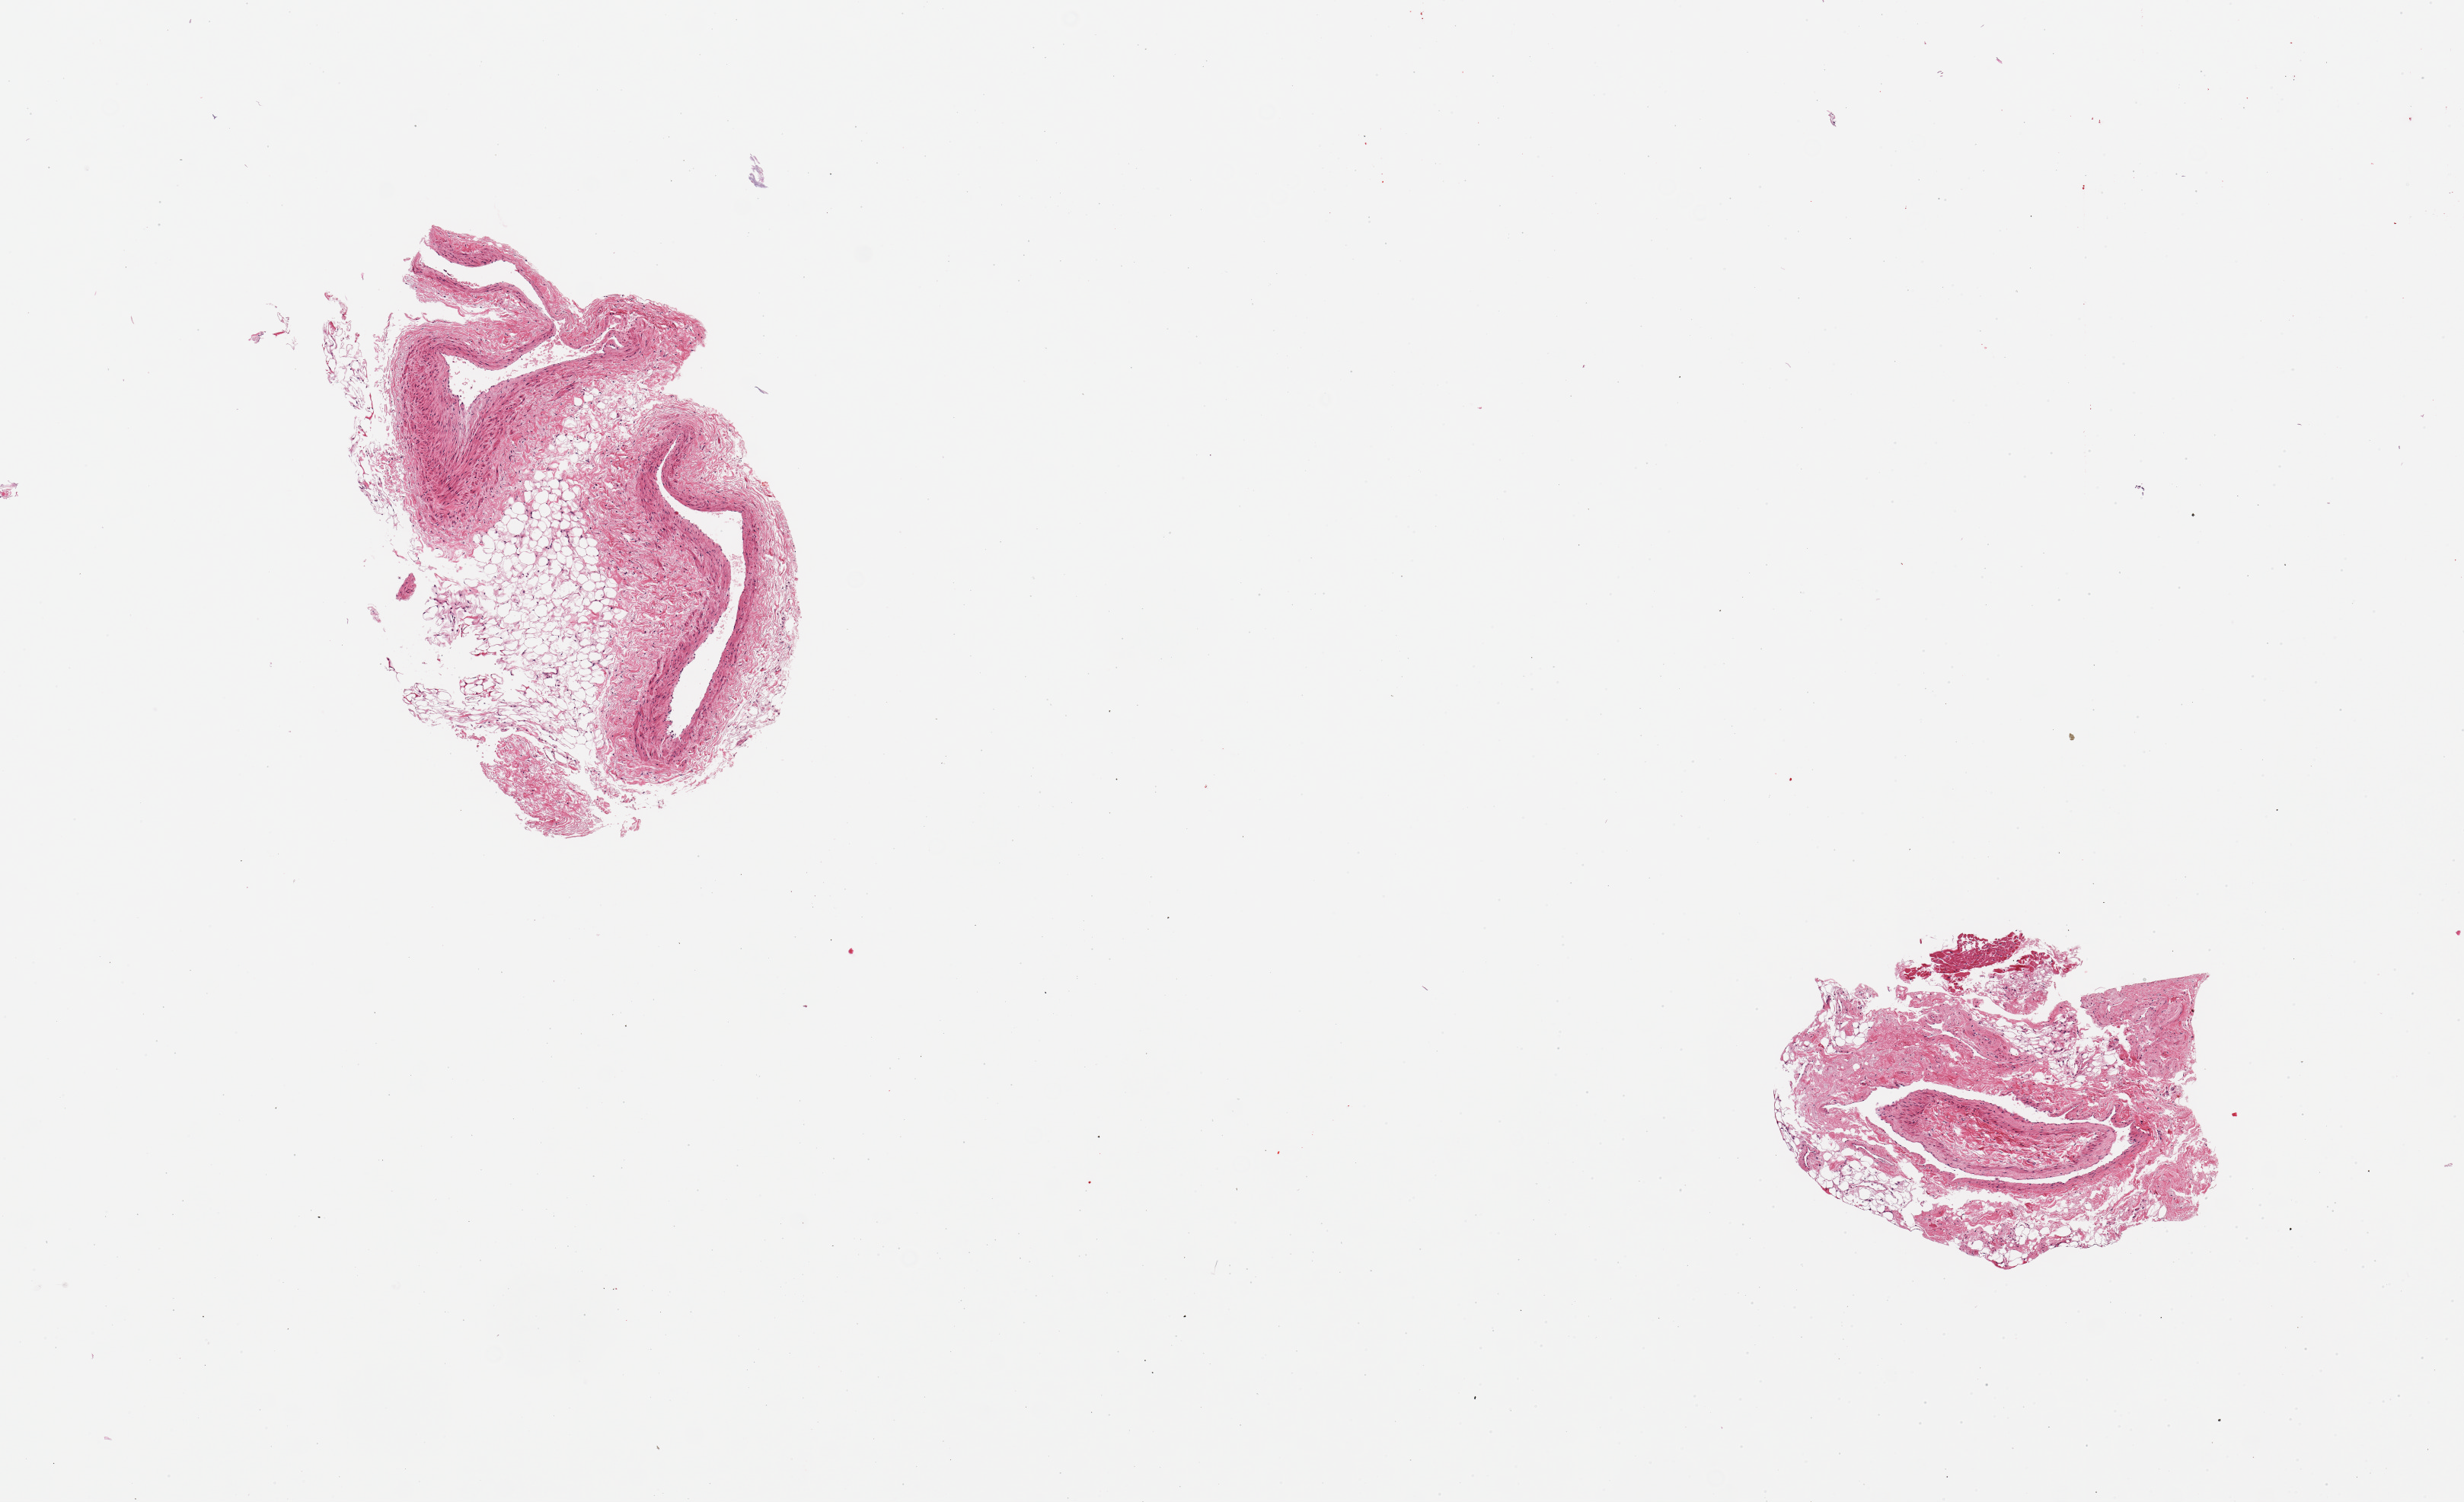
Whole-slide image, haematoxylin and eosin stain, brightfield — low-resolution overview of the scanned area, about 12.8 x 7.8 mm (from a 20x scan). PAXgene-fixed, paraffin-embedded tissue. Target tissue: coronary artery. Donor tissue sample. Male donor.
Pathologist's review note for this sample: 2 pieces; vein with adherent fat, connective tissue and myocardium.